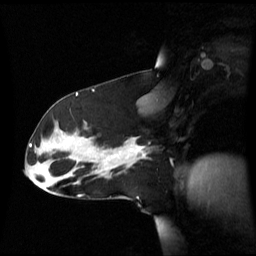
Breast MRI (dynamic contrast-enhanced), one sagittal slice. Position 36 of 60 along the scan axis. Dynamic contrast-enhanced series, image 2 of 3 at this slice position (ordered by acquisition). 1.5 T. TE 4.2 ms, TR 8.4 ms. 2.8 mm slice thickness. 256 × 256 image matrix, field of view 270 × 270 mm. Female patient, age 39 years. Case-level facts recorded for this patient, not image findings: setting: breast cancer imaged before/during neoadjuvant chemotherapy; receptor status: triple-negative.
Outlined on this slice (semi-automatically segmented with operator editing):
- analysis volume of interest (the breast-tissue region the enhancement analysis was run in; not a lesion): bounding box [x1, y1, x2, y2] px = [101, 137, 147, 173]
- tumour enhancement mask (voxels above the 70 % enhancement threshold inside the analysis volume of interest): [127, 146, 145, 157]